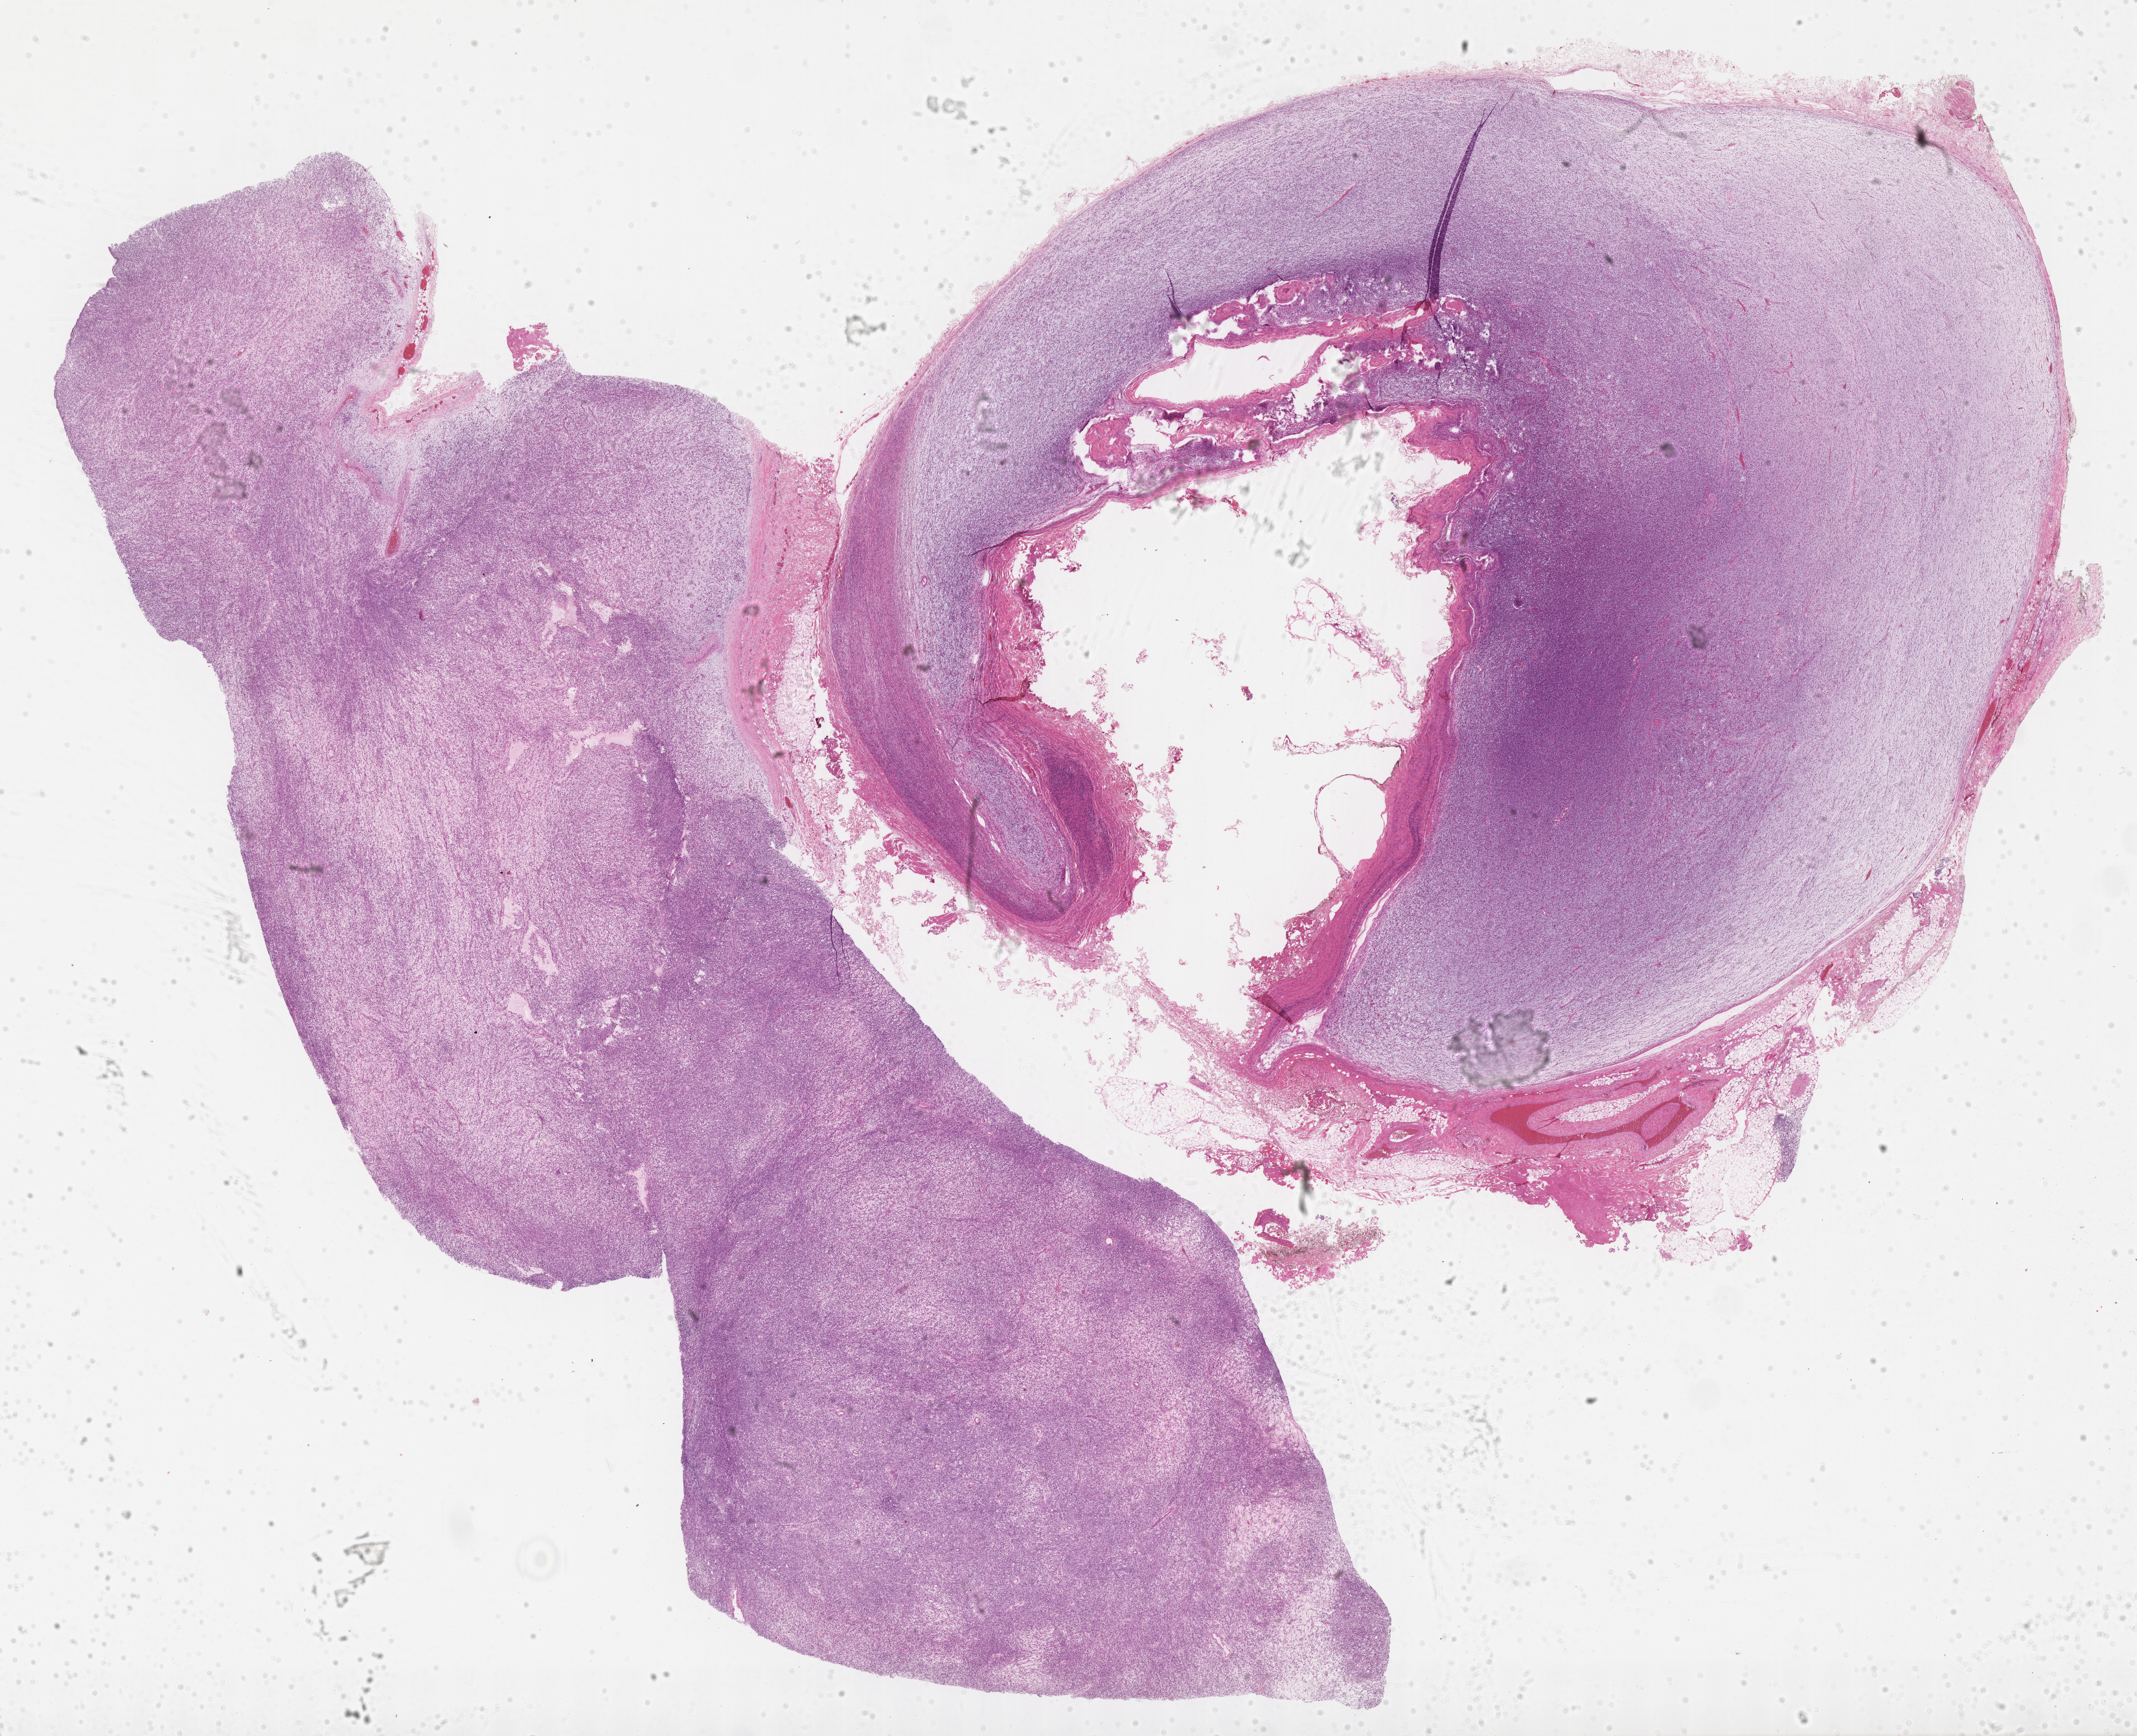
Whole-slide image, H&E stain of tumor tissue, a low-resolution overview of the entire scanned area, about 26.7 x 21.7 mm; FFPE section; sample anatomic site: soft tissue - neck, right. Male patient, age at diagnosis 4.2 years.
- stage (as recorded): 1
- metastatic status at presentation (as recorded): non-metastatic
- diagnosis: rhabdomyosarcoma; histological classification: embryonal rhabdomyosarcoma